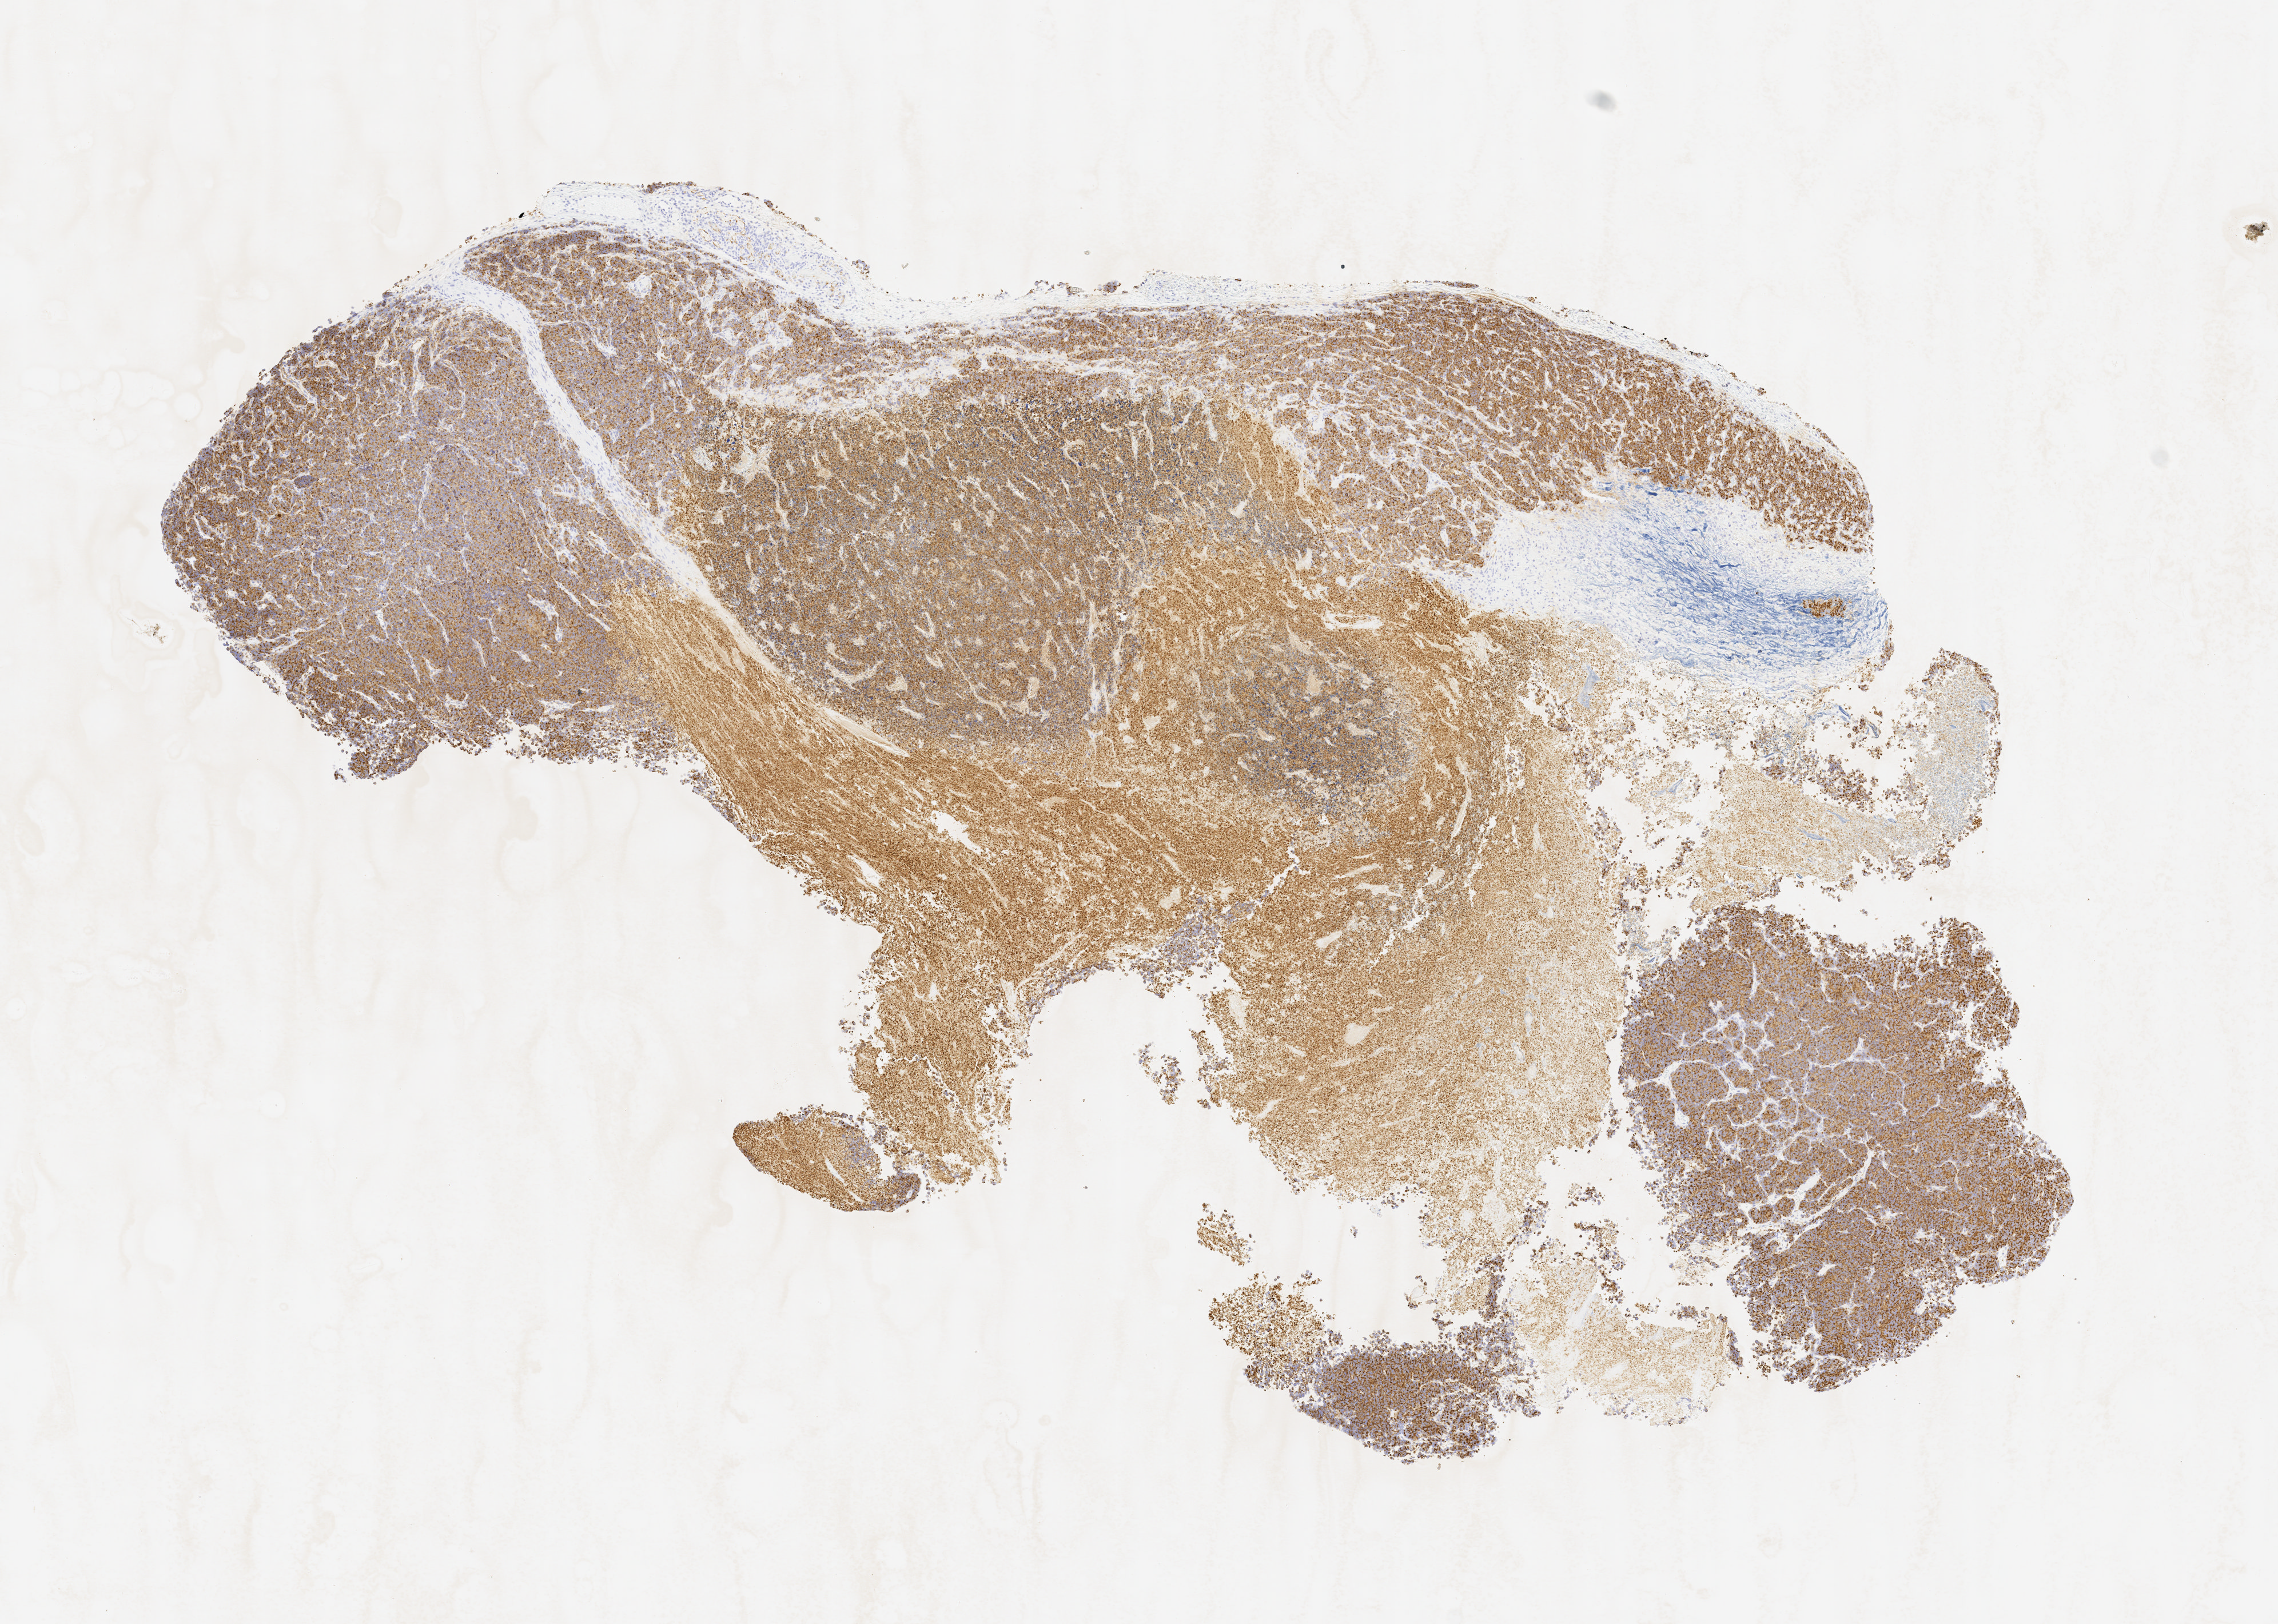
Haematoxylin and eosin whole-slide image of a patient-derived xenograft (PDX) tumor grown in a mouse, passage 0 — whole scanned area (about 8.0 x 5.7 mm) shown as a low-resolution overview. Formalin-fixed paraffin-embedded section. Tumor site category: musculoskeletal.
Originating patient diagnosis: Ewing Sarcoma|Primitive Neuroectodermal Tumor.